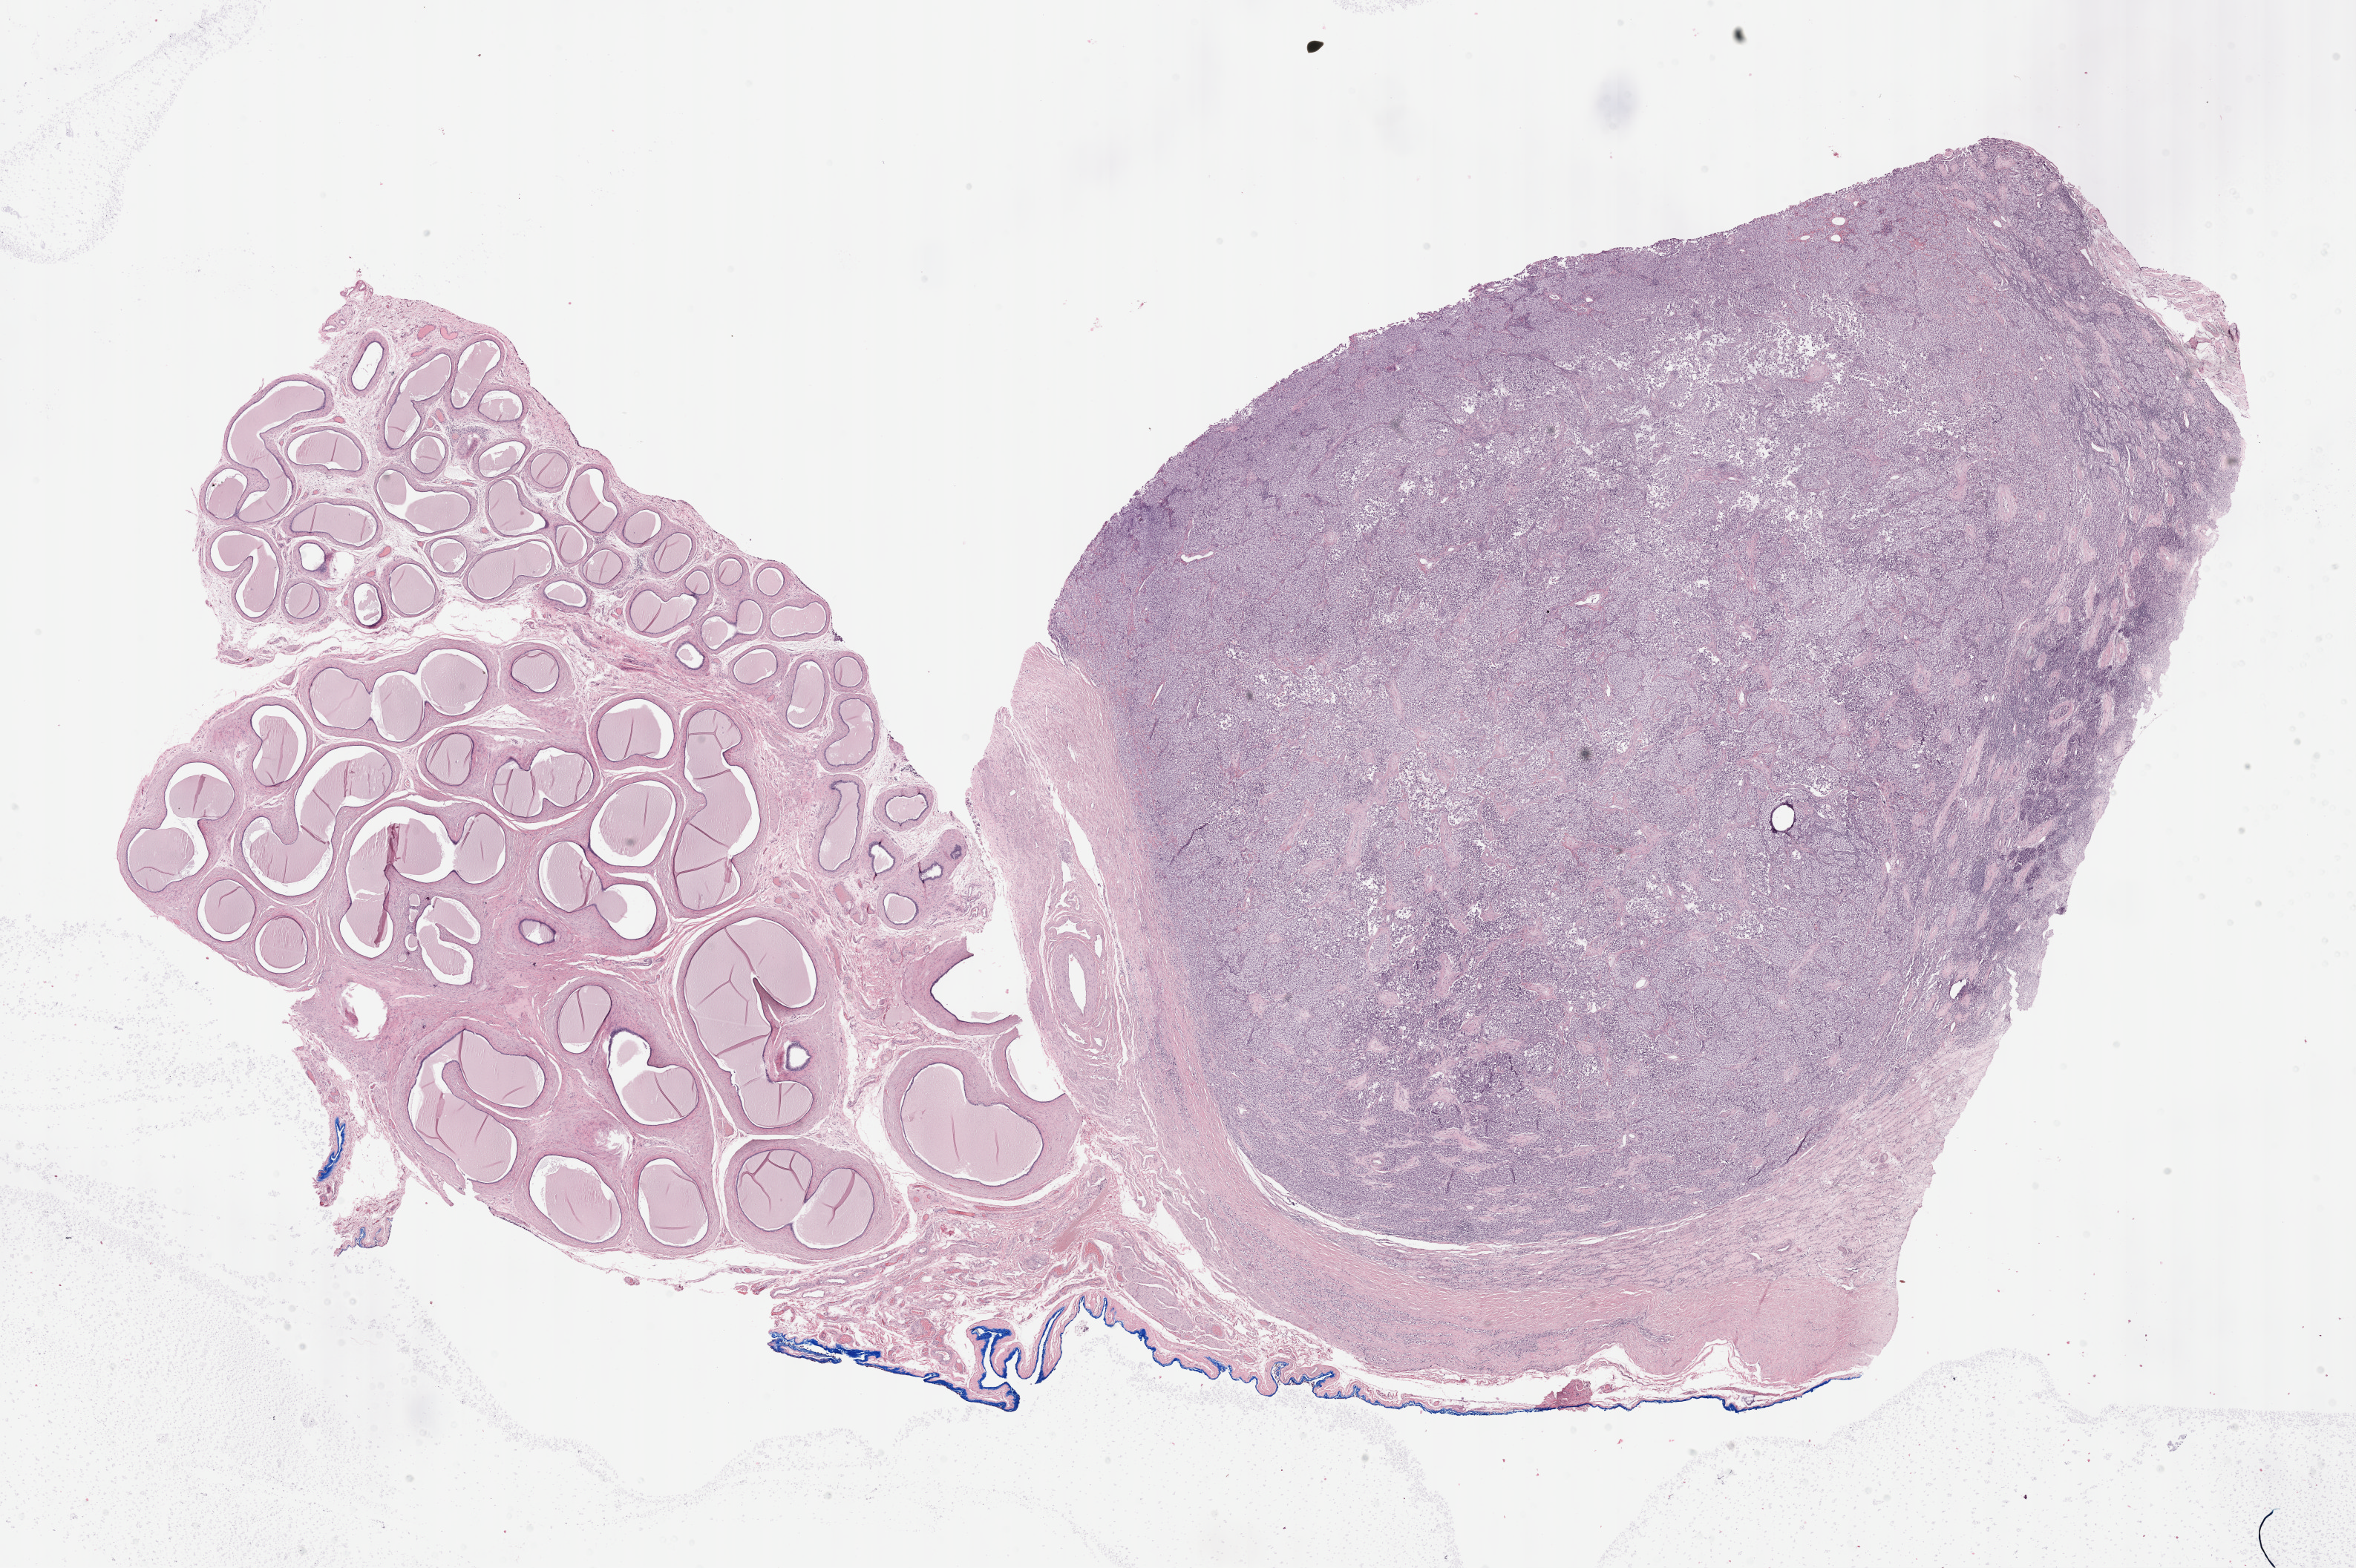
Digitized Hematoxylin and eosin (H&E) stained tissue section (whole slide) — whole scanned area (about 25.7 x 17.1 mm) shown as a low-resolution overview, formalin-fixed paraffin-embedded (FFPE) diagnostic section, testis, primary tumour sample. Male, age 51 years at initial diagnosis.
TNM: T1 N0 M0. AJCC pathologic stage: I (7th edition). Pathologic diagnosis: Seminoma, NOS.